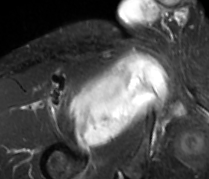
MRI of an extremity soft-tissue mass, one axial slice. Slice 65 of 89 in the series (ordered by position). STIR. MR volume resampled by the dataset authors to the PET/CT grid (not the native acquisition matrix). 209 × 179 image matrix, field of view 204 × 175 mm. Male patient. From the clinical record (not read from this slice): histological type: undifferentiated - pleiomorphic; grade: high; site of the primary tumour: right thigh.
Annotated regions visible in this slice (expert contour drawn on MRI and transferred to this co-registered scan by the dataset authors):
- gross tumour volume including surrounding oedema: bounding box [x1, y1, x2, y2] px = [69, 51, 166, 149]
- gross tumour volume (mass): [69, 53, 166, 149]